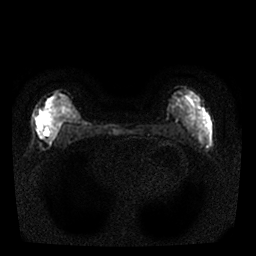
Breast MRI, one axial slice. Position 8 of 25 along the scan axis. Diffusion-weighted series; image 2 of 4 stored at this slice position (different b-values; order by instance number). 1.5 T. 4 mm slice thickness. 256 × 256 image matrix. Female patient.
Structures marked on this image (expert manual segmentation):
- tumour on diffusion-weighted imaging: bounding box <36,114,61,144> (left, top, right, bottom; pixels)